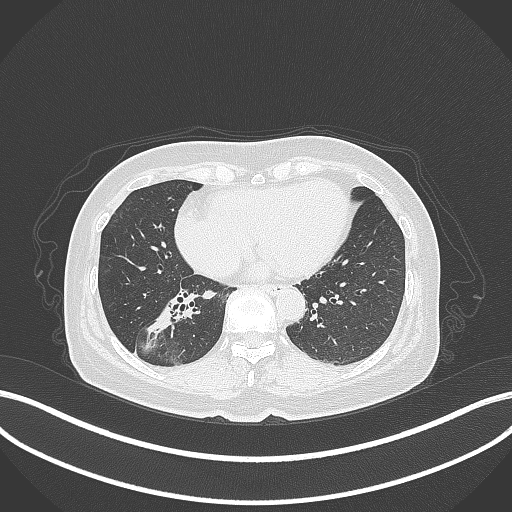
Chest CT, one axial slice; slice 146 of 429 in the series (ordered by position); reconstruction kernel B70f; lung window (W 1500 / L -600 HU); 1 mm slice thickness; 512 × 512 image matrix, field of view 400 × 400 mm. Female patient, age 67 years. Case-level facts recorded for this patient, not image findings: clinical TNM (as recorded): T1c N1 M0; histopathological grade: G2-3.
Structures marked on this image (bounding box drawn by a radiologist):
- lung tumour (recorded histology: adenocarcinoma): box from (x=143, y=289) to (x=201, y=340) px